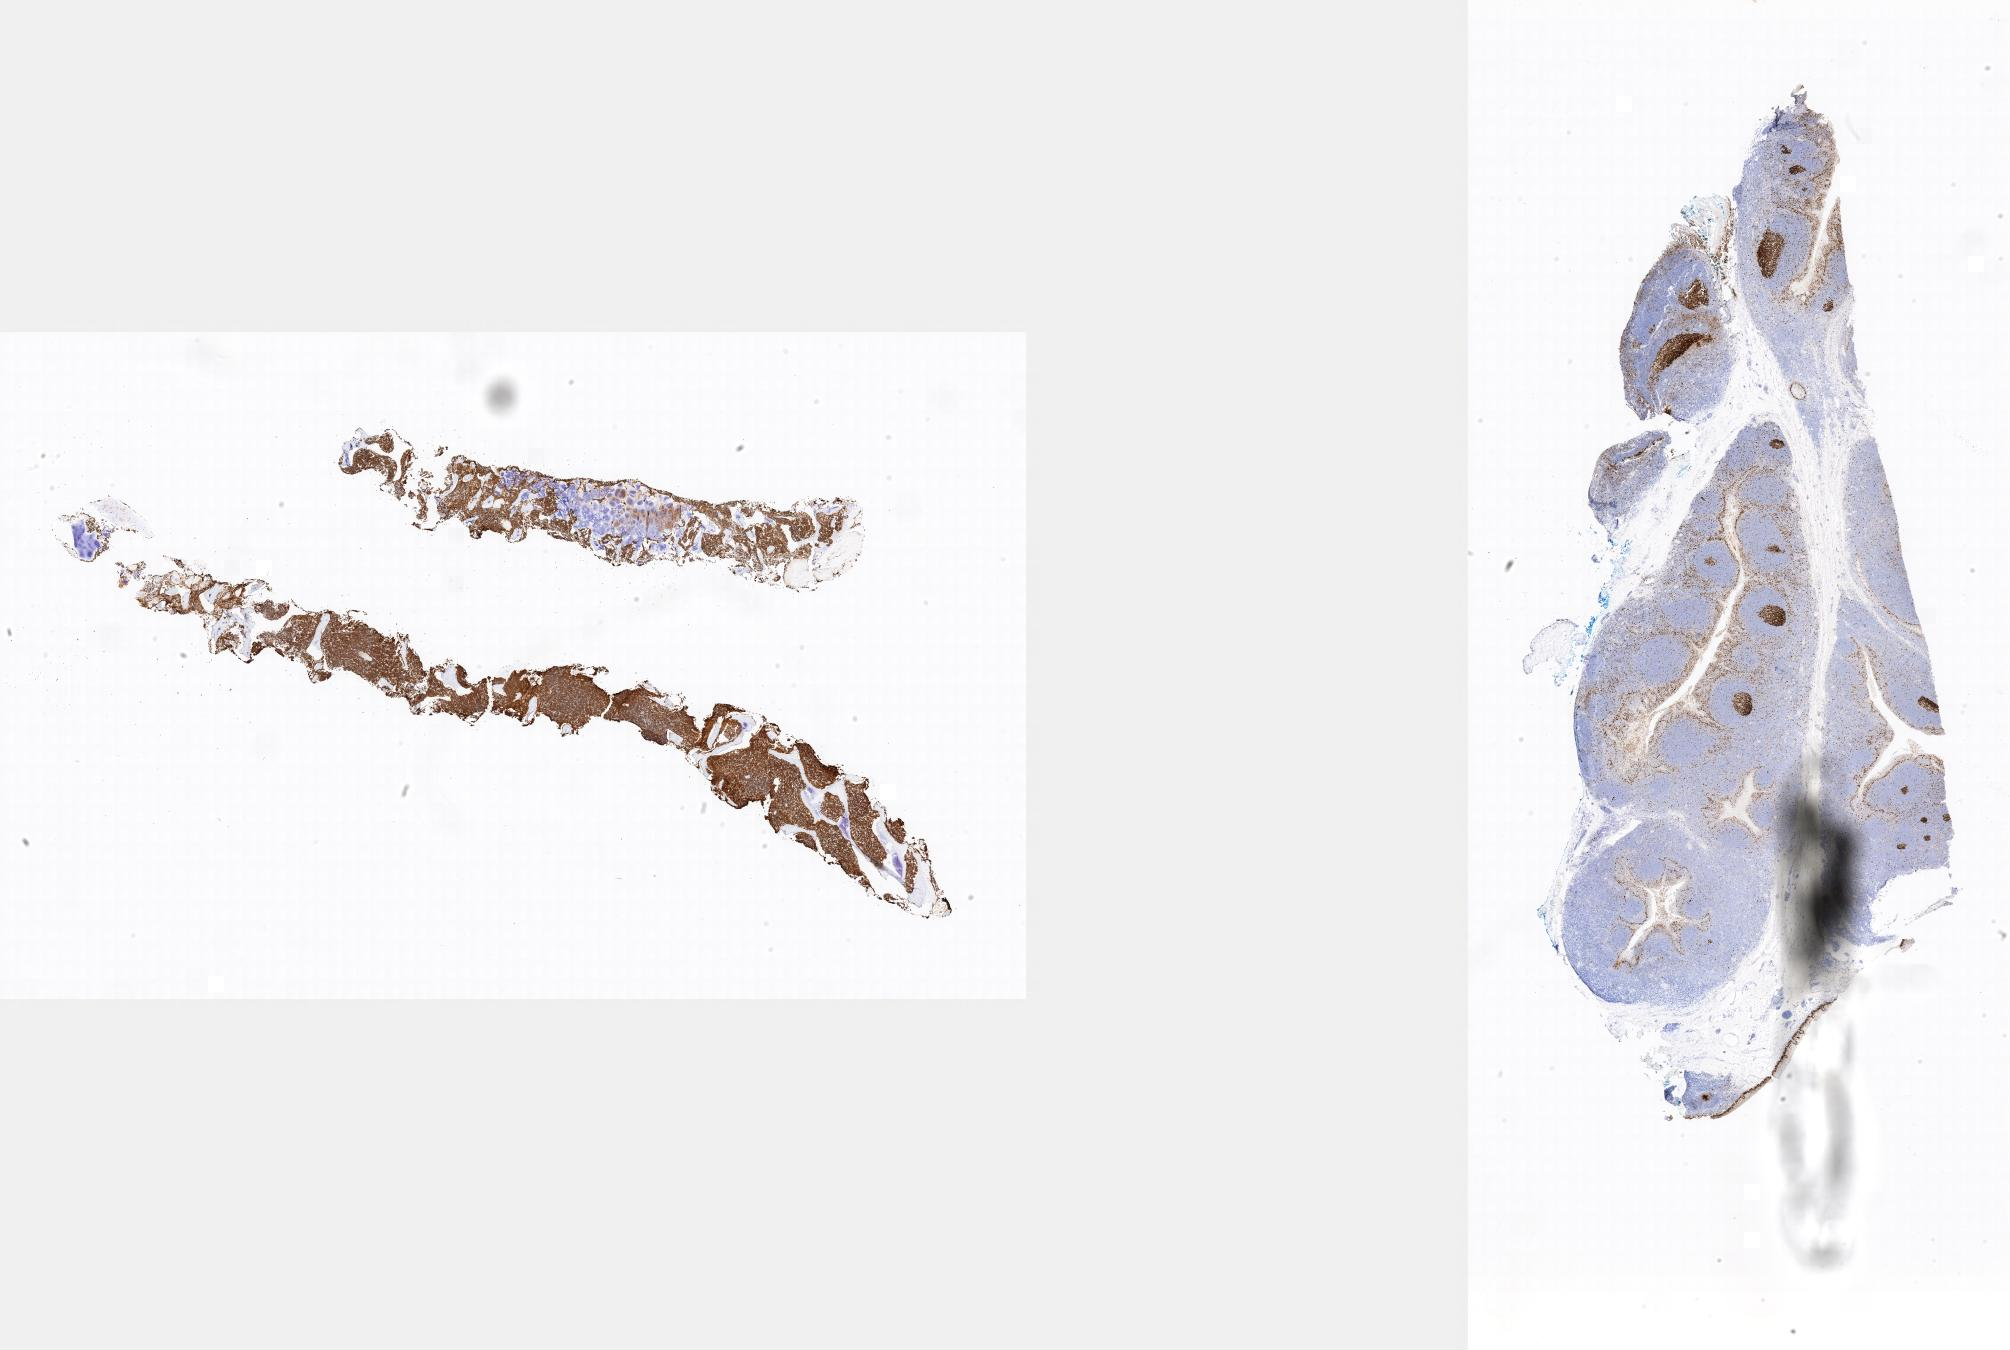
Immunohistochemistry (IHC) whole-slide image stained for Ki-67 — a low-resolution overview of the entire scanned area, specimen: tumor tissue, site: bone marrow. Patient: male, 11 years old.
Histologic diagnosis: Burkitt lymphoma, NOS.